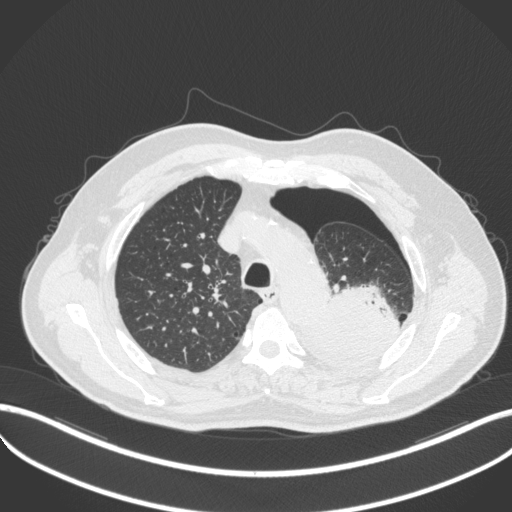
Chest CT, one axial slice. Position 387 of 466 along the scan axis. Lung window (W 1500 / L -600 HU). 1 mm slice thickness. 512 × 512 image matrix, field of view 400 × 400 mm. Patient: male, 76 years. Case-level facts recorded for this patient, not image findings: clinical TNM (as recorded): T3 N0 M1b.
Annotated regions visible in this slice (bounding box drawn by a radiologist):
- lung tumour (recorded histology: adenocarcinoma): bounding box [x1, y1, x2, y2] px = [295, 278, 396, 368]